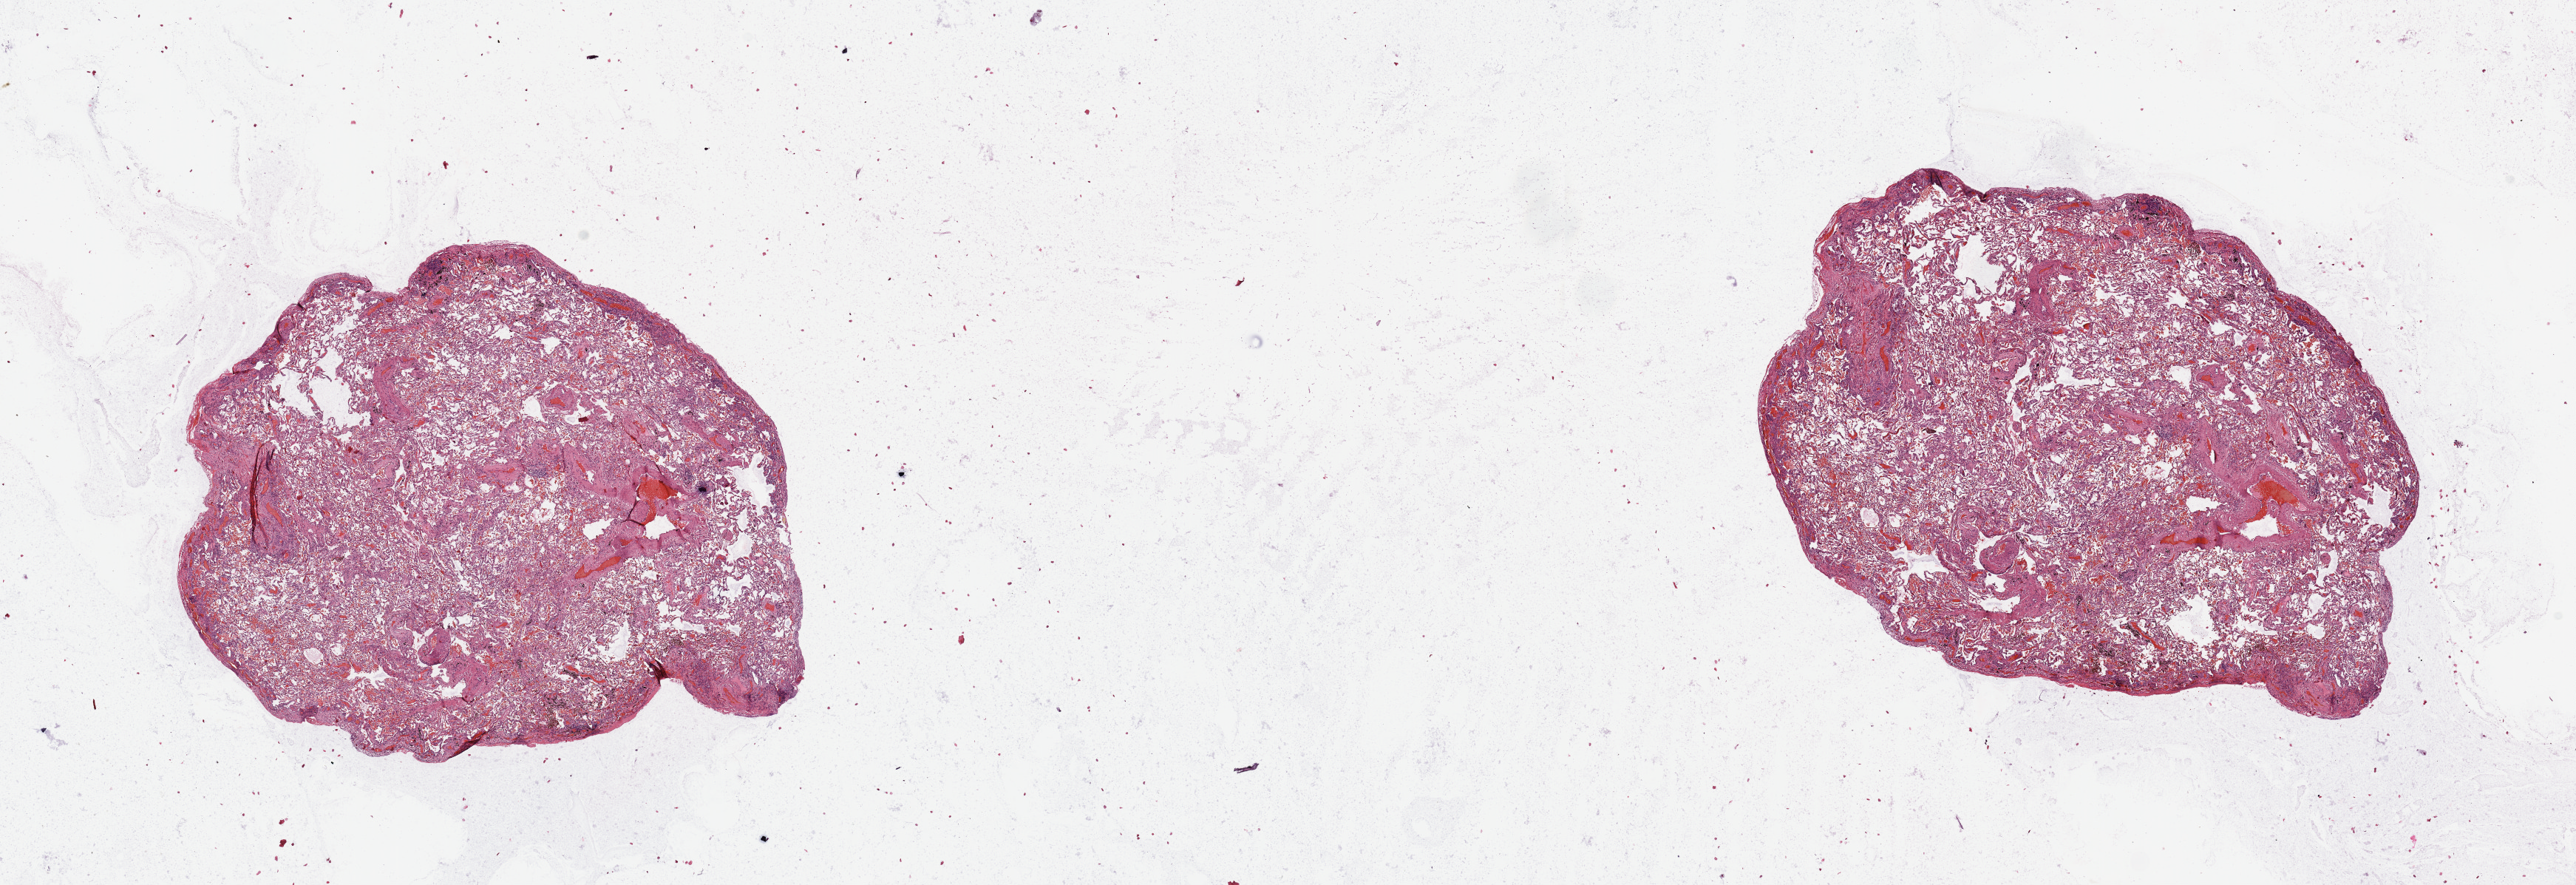
H&E-stained whole-slide image, whole scanned area (about 27.6 x 9.5 mm, acquisition: 20x scan) shown as a low-resolution overview; normal (non-tumour) tissue sample, lung. Patient: male, age 72 years.
This section: normal (non-tumour) tissue from the same patient. Patient diagnosis: Squamous cell carcinoma, NOS.